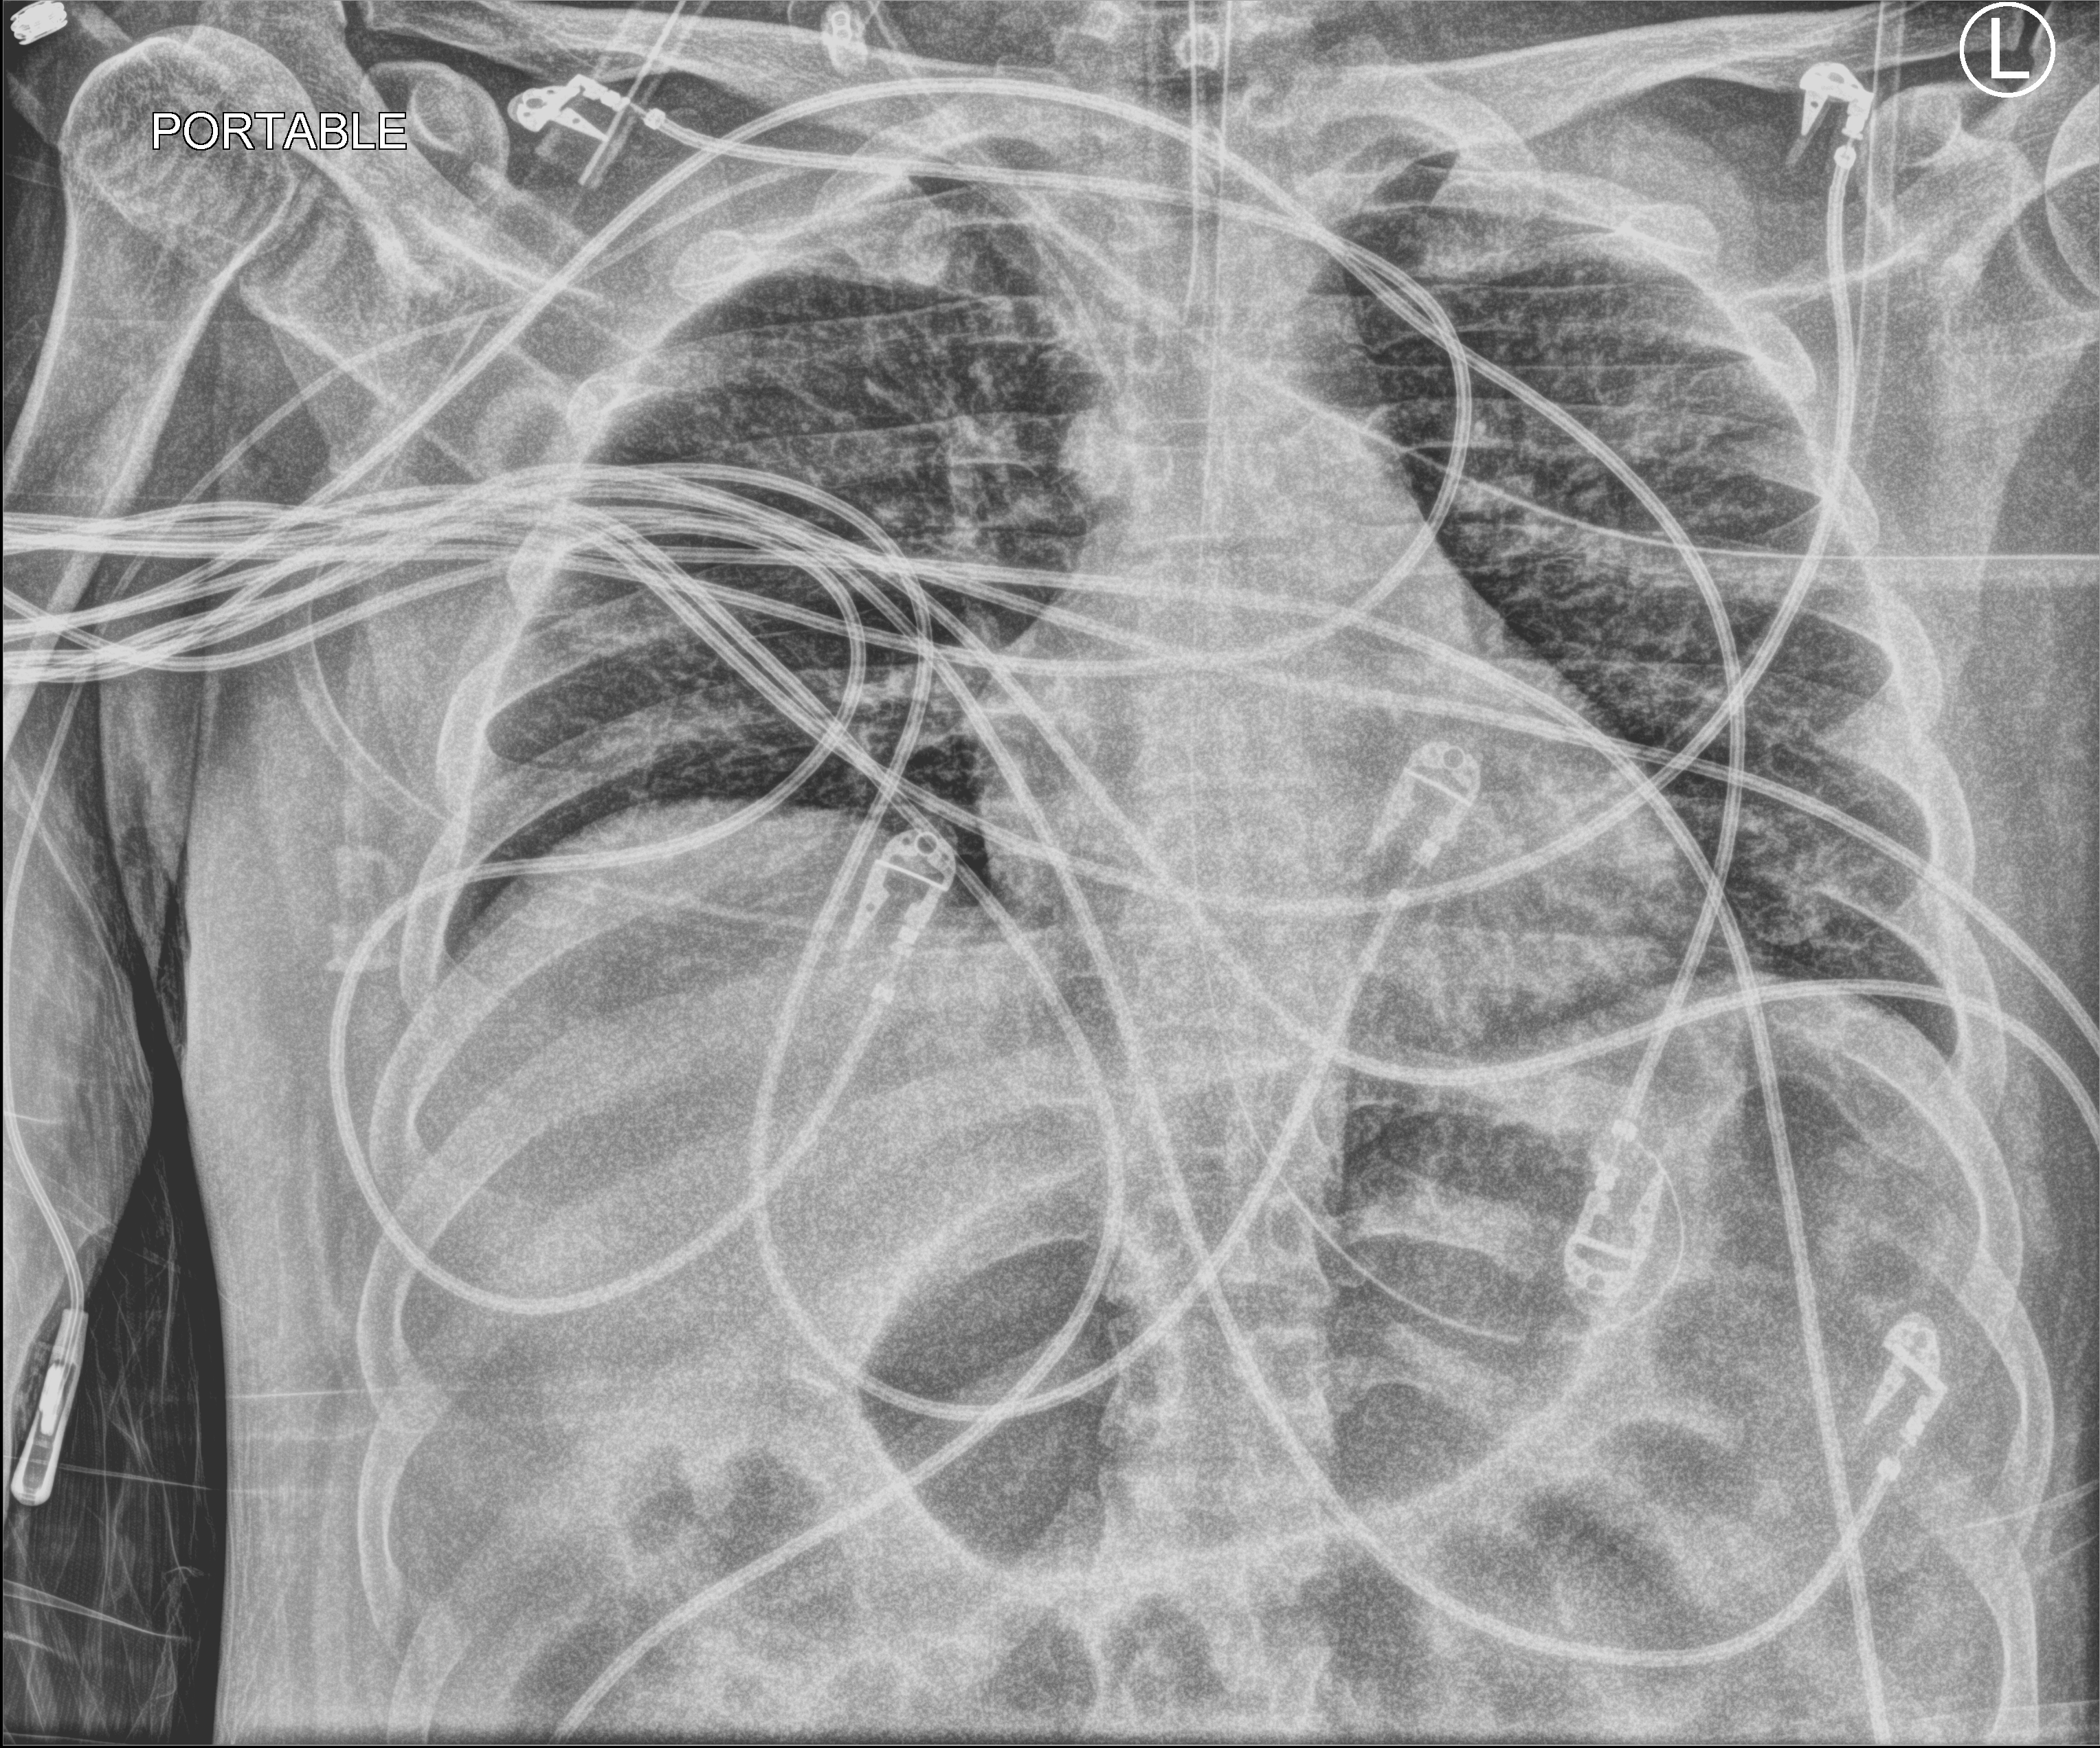
Portable chest radiograph, anteroposterior (AP) projection. Male patient hospitalised with COVID-19, age 18–59 years.
Hospital-stay facts (about this admission, not read from this image; timing relative to this image not recorded): admitted to intensive care during this hospital stay: yes; mechanically ventilated during this hospital stay: yes.